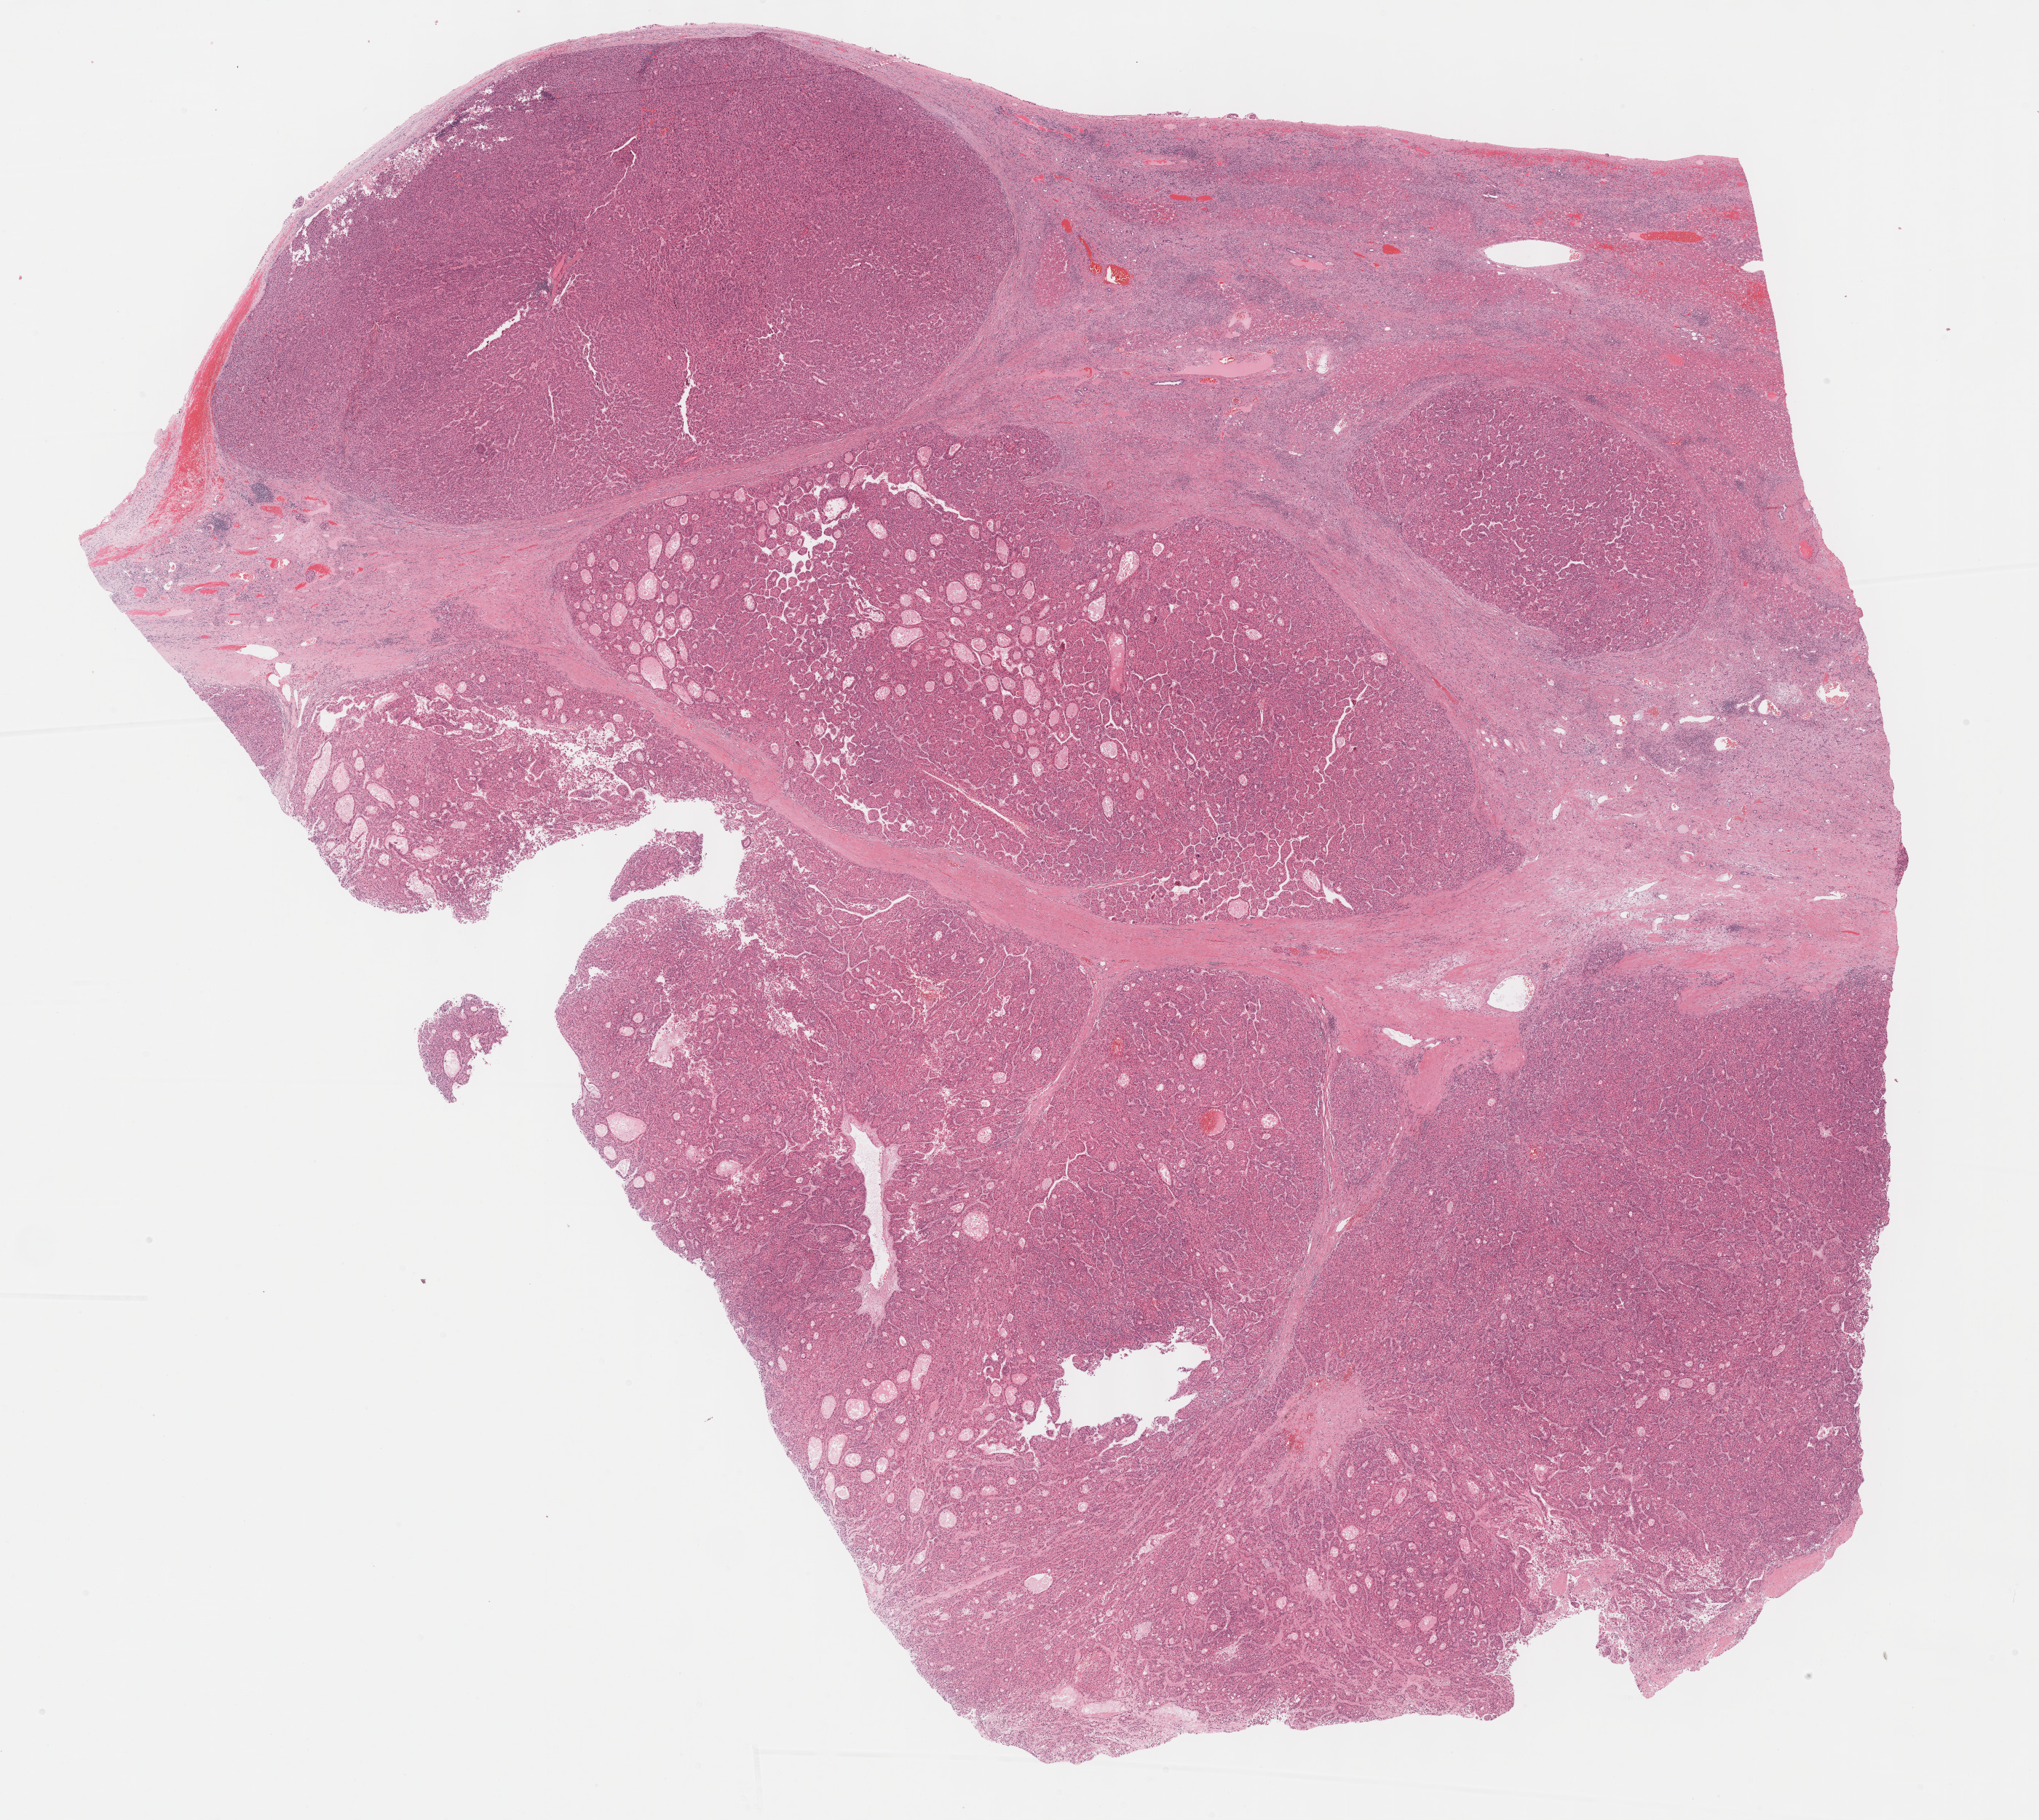
H&E-stained whole-slide image — low-resolution overview of the scanned area, about 22.7 x 20.2 mm, formalin-fixed paraffin-embedded (FFPE) diagnostic section, sample: primary tumour, liver. Patient: male, age at initial diagnosis 64 years. Histologic grade: G2 (moderately differentiated).
Diagnosis: Hepatocellular carcinoma, NOS. AJCC pathologic stage: I (6th edition).